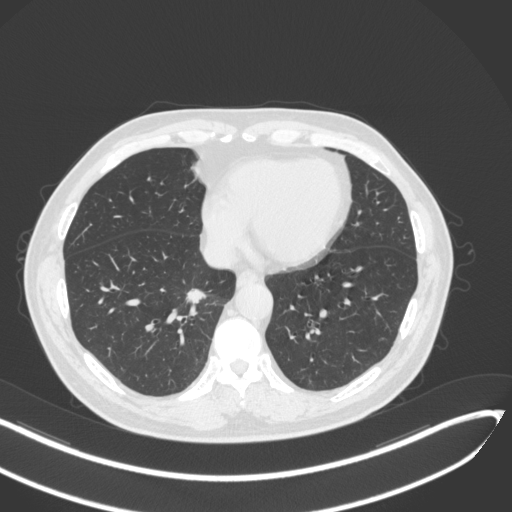
Chest CT, one axial slice. Position 125 of 429 along the scan axis. 120 kVp. Lung window (W 1500 / L -600 HU). 1 mm slice thickness. 512 × 512 image matrix, field of view 400 × 400 mm. Patient: male, 62 years. Case-level facts recorded for this patient, not image findings: clinical TNM (as recorded): T1b N0 M0; histopathological grade: G2.
Annotated regions visible in this slice (bounding box drawn by a radiologist):
- lung tumour (recorded histology: adenocarcinoma): bounding box <182,284,217,310> (left, top, right, bottom; pixels)